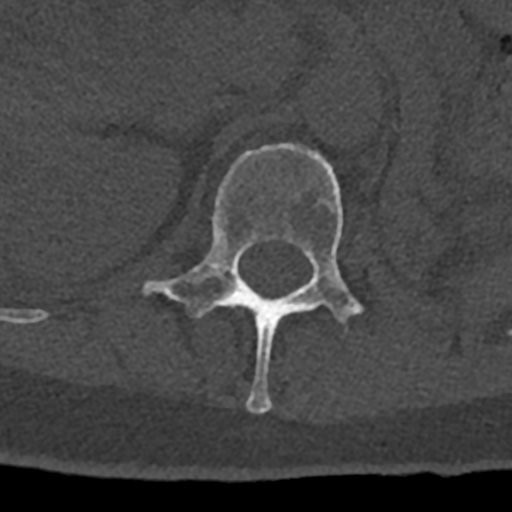
CT including the spine, one axial slice; position 439 of 797 along the scan axis; bone window (W 1800 / L 400 HU); 0.5 mm slice thickness; 512 × 512 image matrix, field of view 160 × 160 mm. Patient: male, 74 years. From the clinical record (not read from this slice): primary cancer: renal.
Annotated regions visible in this slice (semi-automatically segmented with operator editing):
- L1 vertebra: bounding box (x1, y1, x2, y2) in pixels: (142, 143, 364, 414)